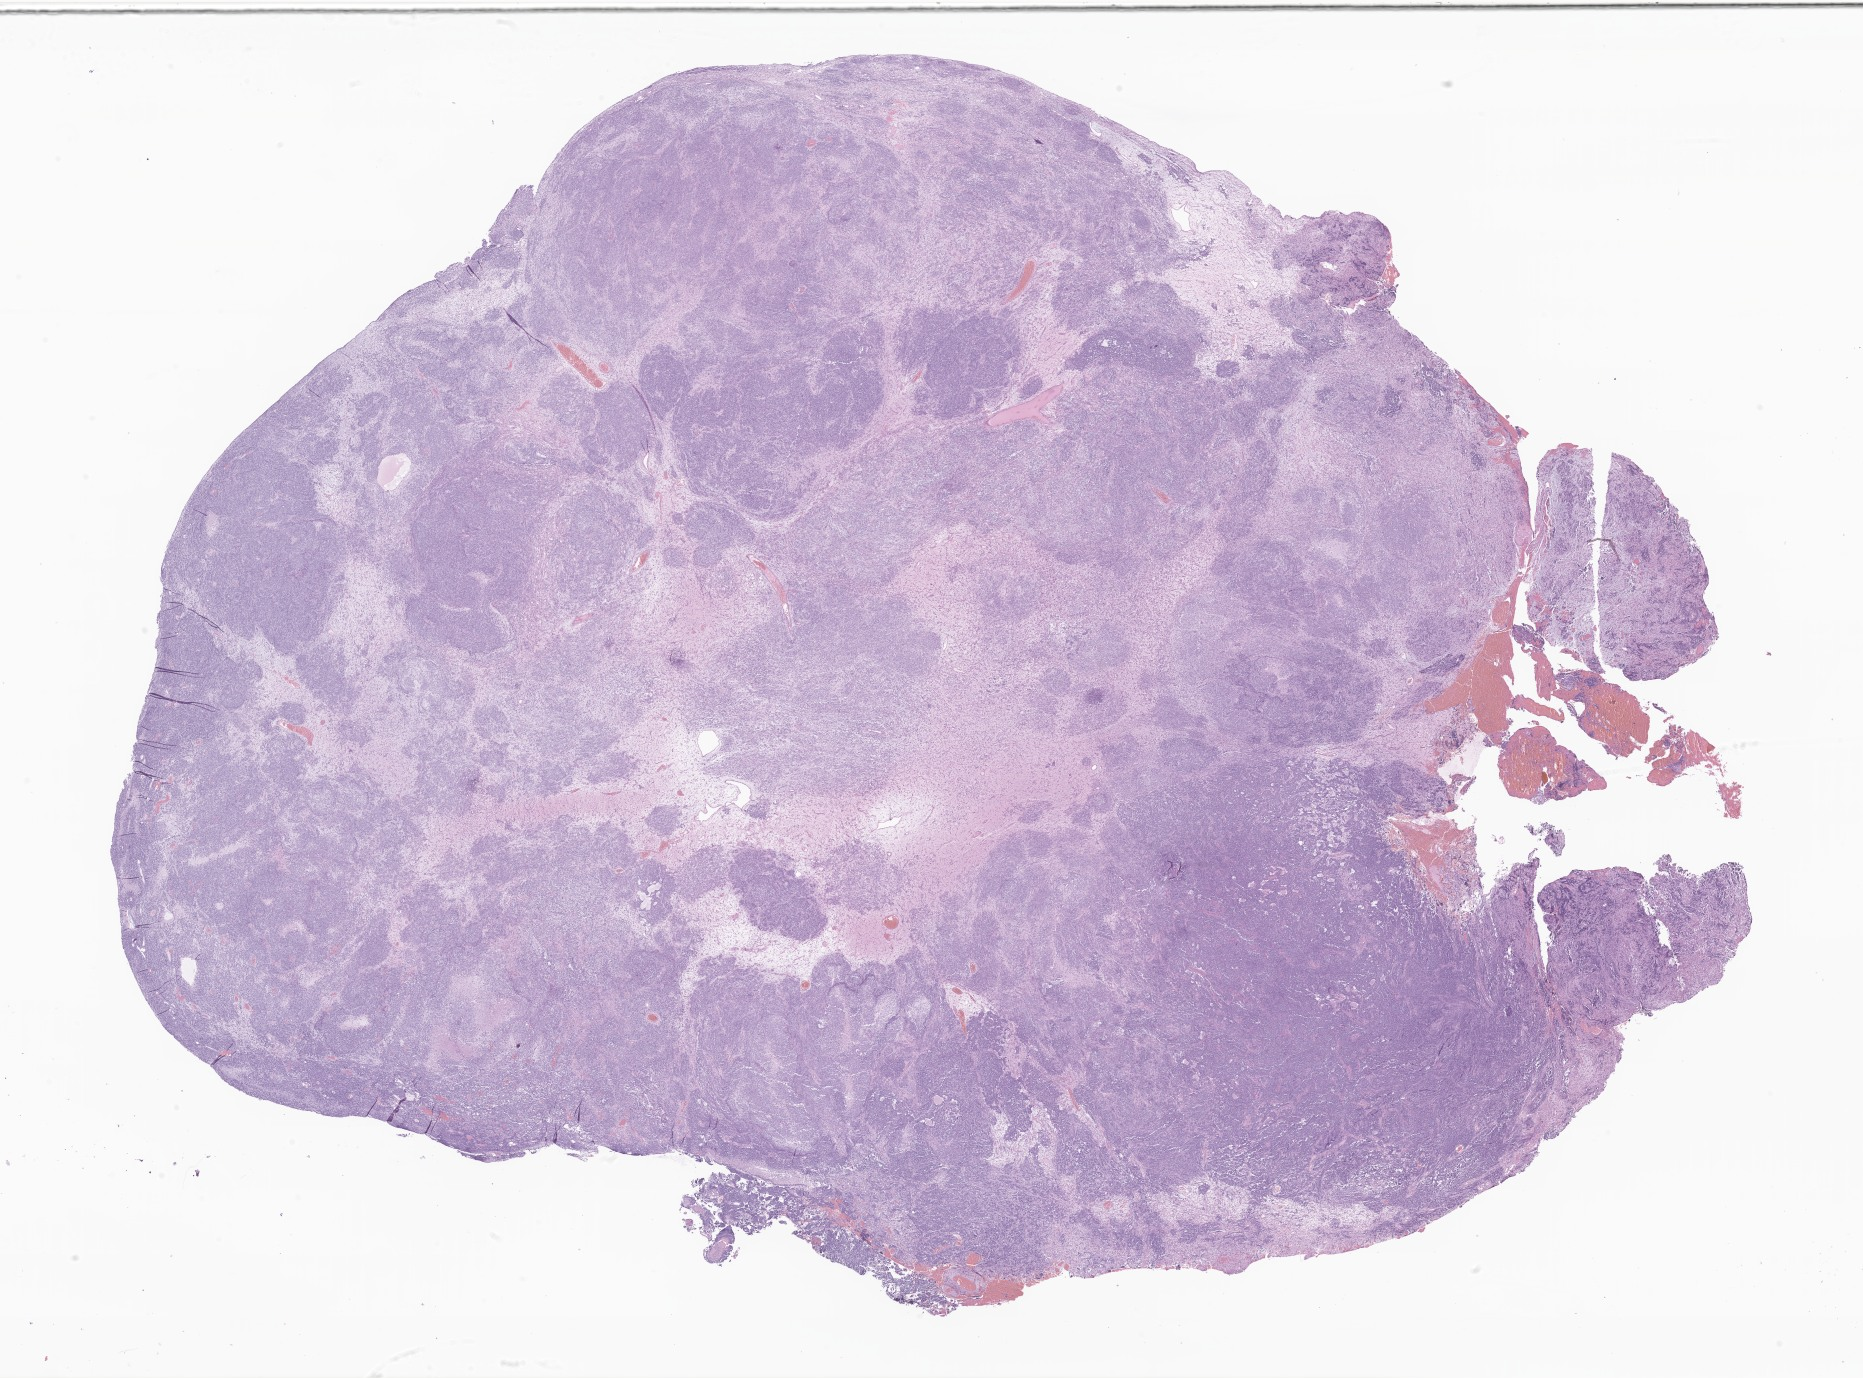
Digitized haematoxylin and eosin-stained section of tumor tissue from the cerebral ventricle, low-resolution overview of the scanned area, about 31.4 x 23.2 mm; formalin-fixed, paraffin-embedded (FFPE) tissue. Patient: male, age 60 months (5 years).
- recorded diagnosis: Medulloblastoma, NOS